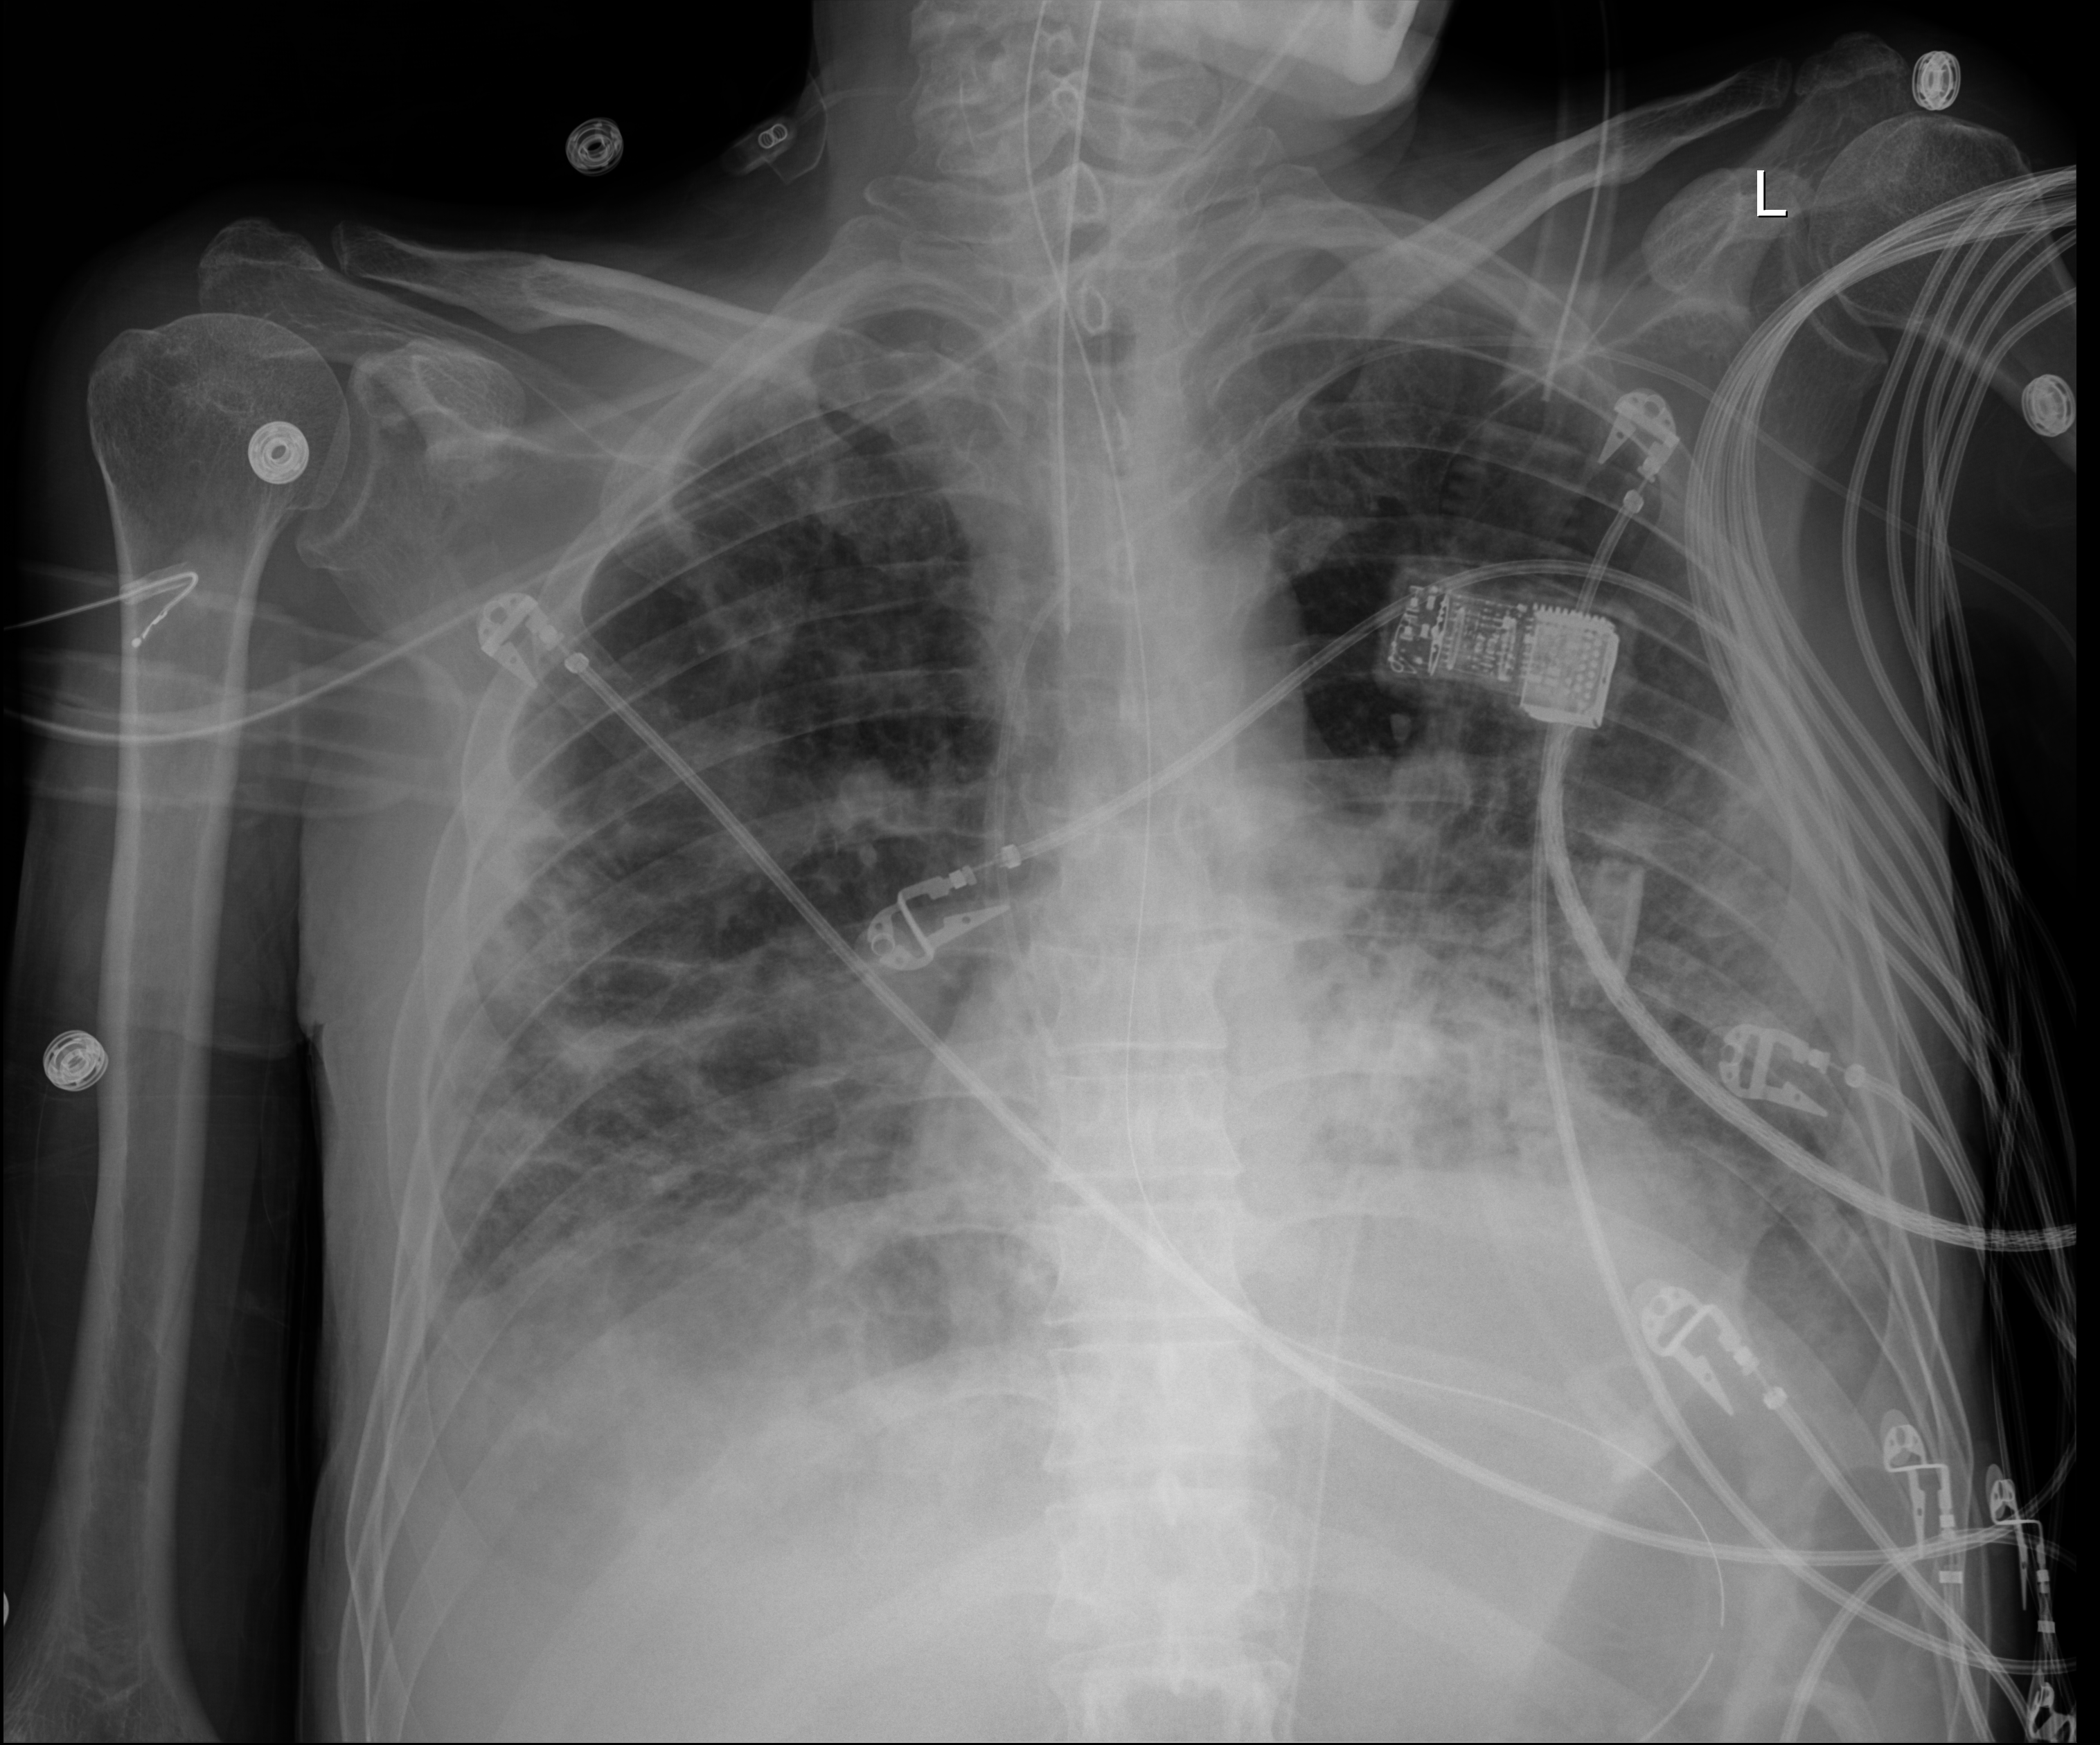
Chest X-ray (portable), anteroposterior (AP) projection. Male patient hospitalised with COVID-19, age 18–59 years.
Admission-level facts for this patient (not findings on this image; timing relative to this image not recorded): length of hospital stay: 96 days.